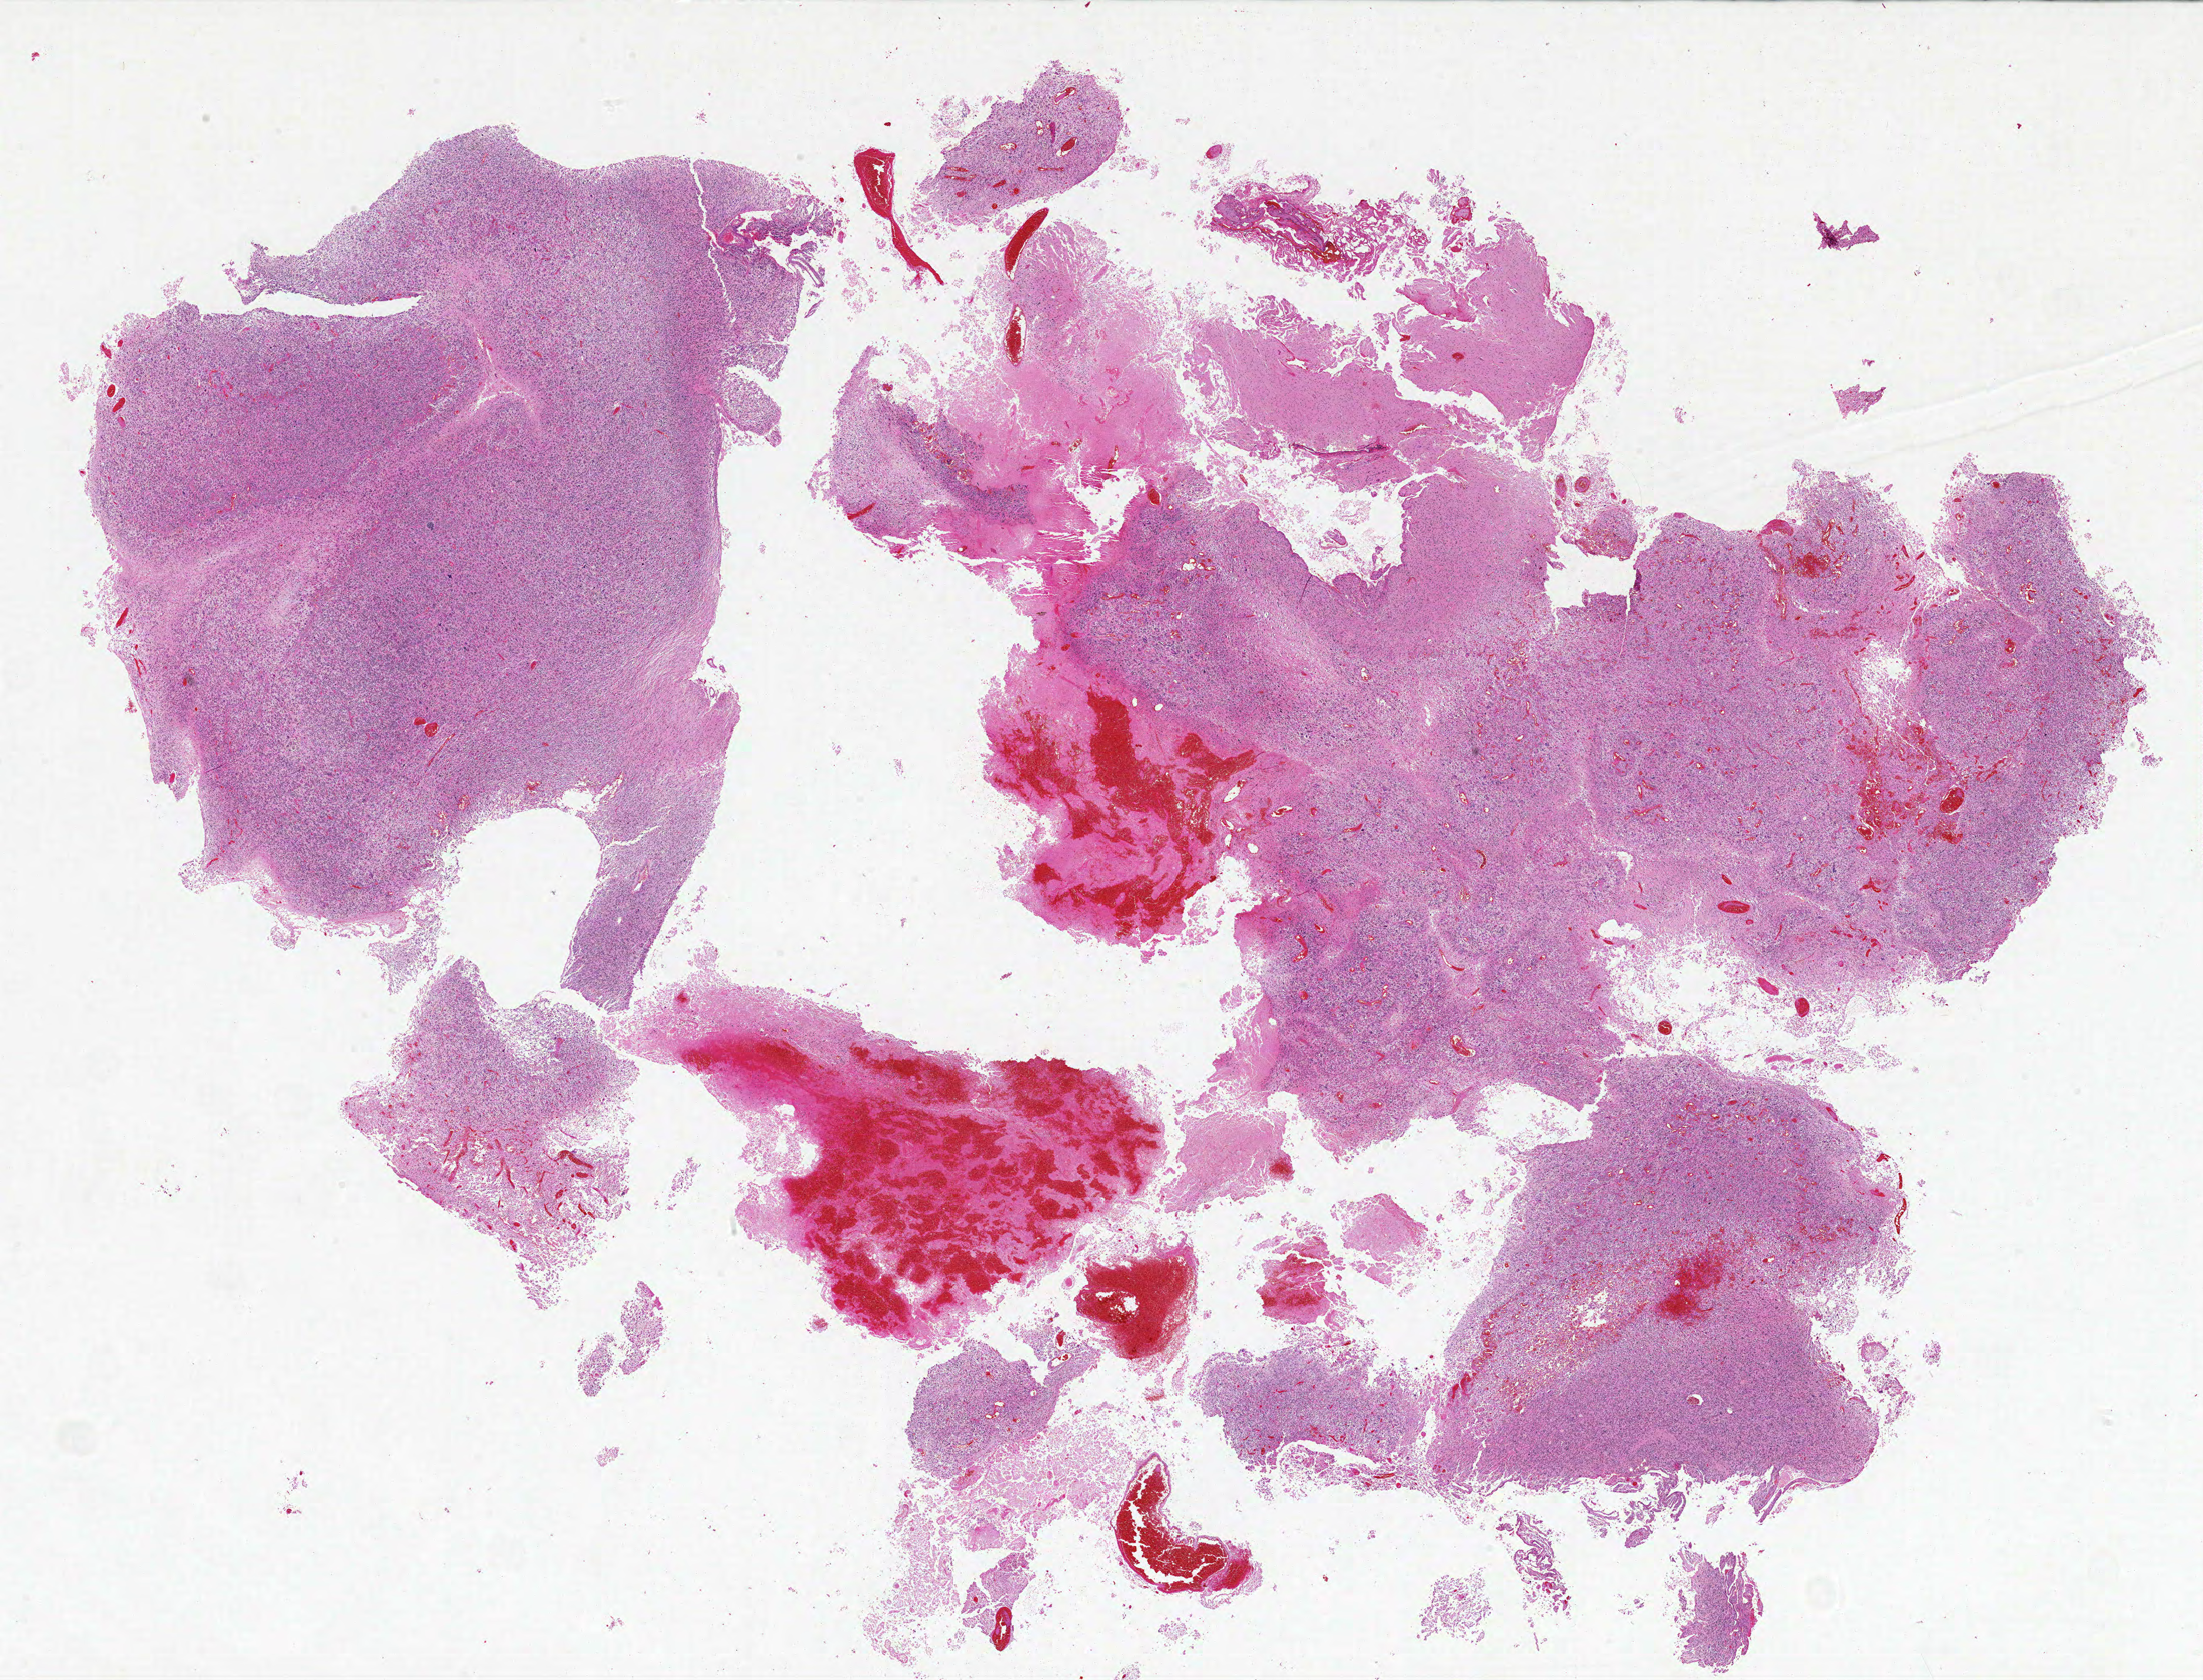
Hematoxylin and eosin (H&E) stained whole-slide image — whole scanned area (about 30.0 x 22.9 mm) shown as a low-resolution overview, formalin-fixed paraffin-embedded (FFPE) diagnostic section, sample: primary tumour, brain. Female, age 59 years at initial diagnosis.
Histologic diagnosis: Glioblastoma.